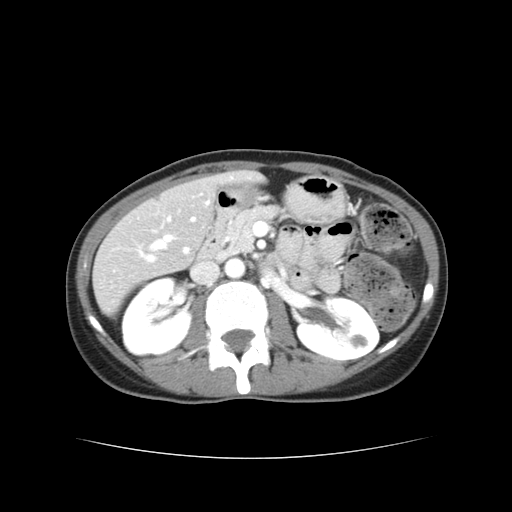
Contrast-enhanced abdominal CT, one axial slice. Position 16 of 38 along the scan axis. Reconstruction kernel STANDARD. 120 kVp. Intravenous contrast given. Soft-tissue window (W 400 / L 40 HU). 5 mm slice thickness. 512 × 512 image matrix, field of view 340 × 340 mm. Female patient, age 54 years. Case-level facts recorded for this patient, not image findings: diagnosis: colorectal cancer liver metastases, imaged before liver resection; multiple liver metastases: yes; largest metastasis: 1.1 cm; disease in both lobes: yes.
Outlined on this slice (expert manual segmentation):
- hepatic veins: bounding box <140,236,172,257> (left, top, right, bottom; pixels)
- liver: <95,173,253,311>
- planned liver remnant (the part of the liver to remain after resection): <224,173,254,181>
- portal vein (with intrahepatic branches): <147,218,195,262>